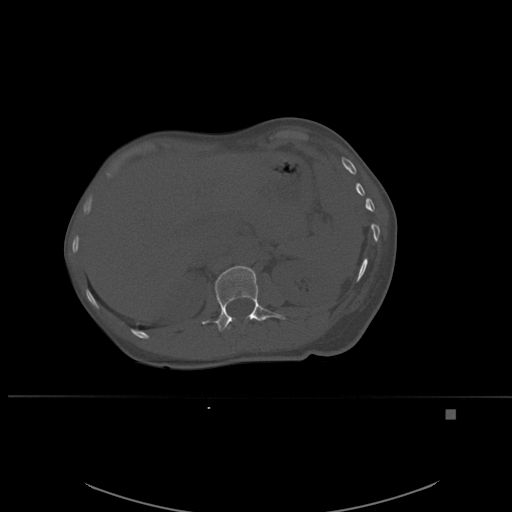
CT including the spine, one axial slice. Position 263 of 537 along the scan axis. Bone window (W 1800 / L 400 HU). 1.5 mm slice thickness. 512 × 512 image matrix. Patient: female, 45 years. Case-level facts recorded for this patient, not image findings: primary cancer: lung.
Outlined on this slice (semi-automatically segmented with operator editing):
- L1 vertebra: bounding box <202,266,286,332> (left, top, right, bottom; pixels)
- T12 vertebra: <228,326,230,329>